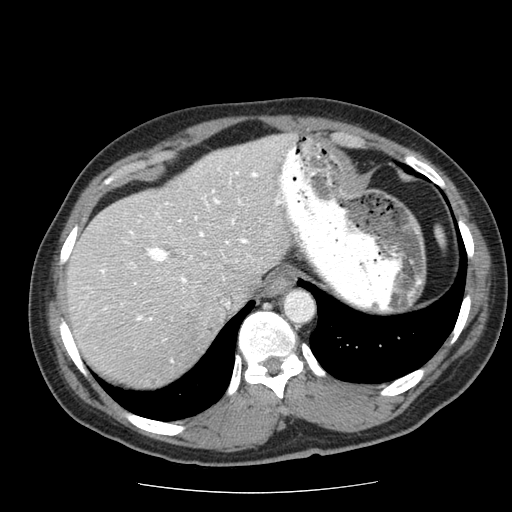
Contrast-enhanced abdominal CT (liver protocol), one axial slice. Position 48 of 85 along the scan axis. Reconstruction kernel STANDARD. 120 kVp. Soft-tissue window (W 400 / L 40 HU). 512 × 512 image matrix, field of view 360 × 360 mm. From the clinical record (not read from this slice): diagnosis: hepatocellular carcinoma (patient treated with transarterial chemoembolisation; whether this scan precedes or follows treatment is not stated here); TNM stage (as recorded): Stage-IIIA.
Annotated regions visible in this slice (semi-automatic segmentation, software-assisted and operator-edited):
- liver parenchyma outside the tumour (the mass and vessels are separate outlines, so this box may not span the whole liver): bounding box (x1, y1, x2, y2) in pixels: (66, 134, 296, 386)
- liver vessels: (86, 167, 282, 362)